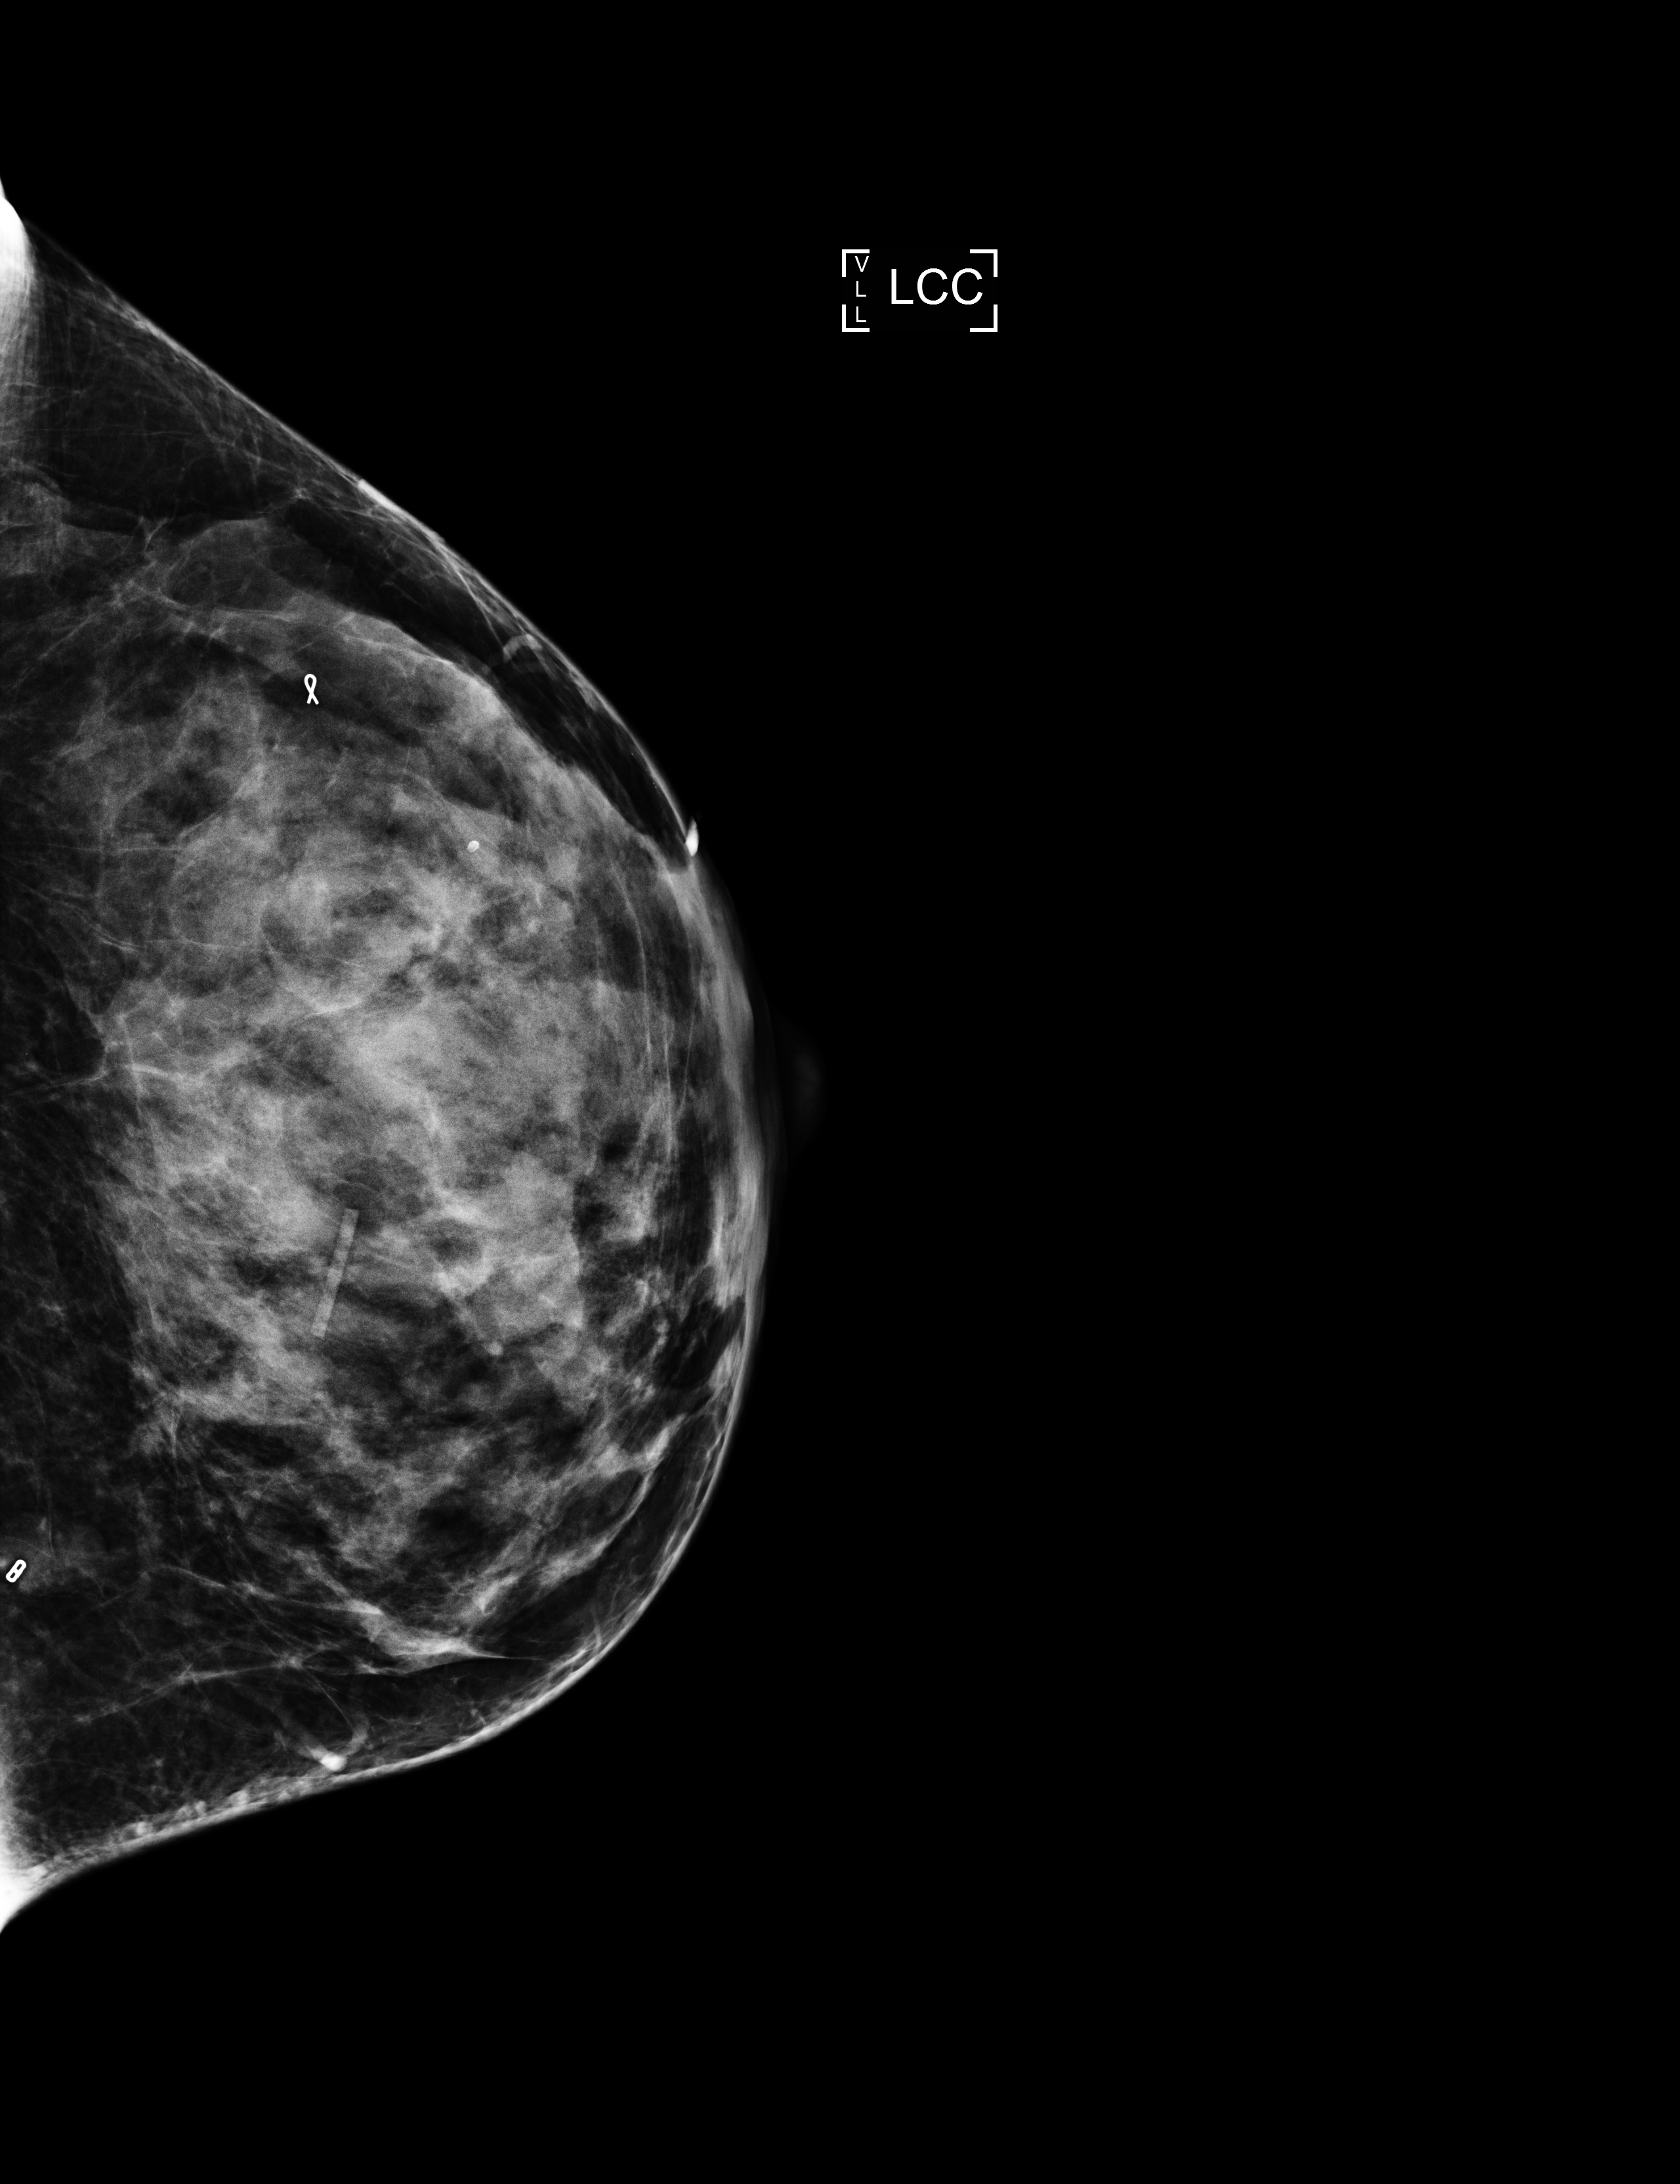
Screening examination; system: Selenia Dimensions. Patient aged 48 years (female).
Image type: full-field digital mammogram. Breast: left. Projection: cranio-caudal projection.